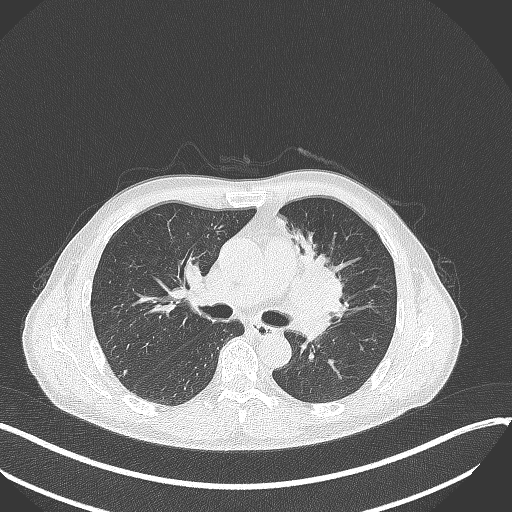
Chest CT, one axial slice. Position 201 of 411 along the scan axis. 120 kVp. Lung window (W 1500 / L -600 HU). 1 mm slice thickness. 512 × 512 image matrix, field of view 400 × 400 mm. Patient: male, 56 years. Case-level facts recorded for this patient, not image findings: clinical TNM (as recorded): T2a N0 M0.
Structures marked on this image (rectangle marked by the reading radiologist):
- lung tumour (recorded histology: squamous cell carcinoma): bounding box <290,229,351,315> (left, top, right, bottom; pixels)